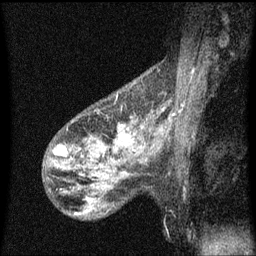
Breast MRI (dynamic contrast-enhanced), one sagittal slice; slice 40 of 60 in the series (ordered by position); dynamic contrast-enhanced series, image 2 of 3 at this slice position (ordered by acquisition); 1.5 T; TE 4.2 ms, TR 8 ms; 256 × 256 image matrix, field of view 200 × 200 mm. Patient: female, 50 years.
Annotated regions visible in this slice (semi-automatically segmented with operator editing):
- analysis volume of interest (the breast-tissue region the enhancement analysis was run in; not a lesion): bounding box (x1, y1, x2, y2) in pixels: (106, 118, 148, 159)
- tumour enhancement mask (voxels above the 70 % enhancement threshold inside the analysis volume of interest): (125, 138, 127, 141)